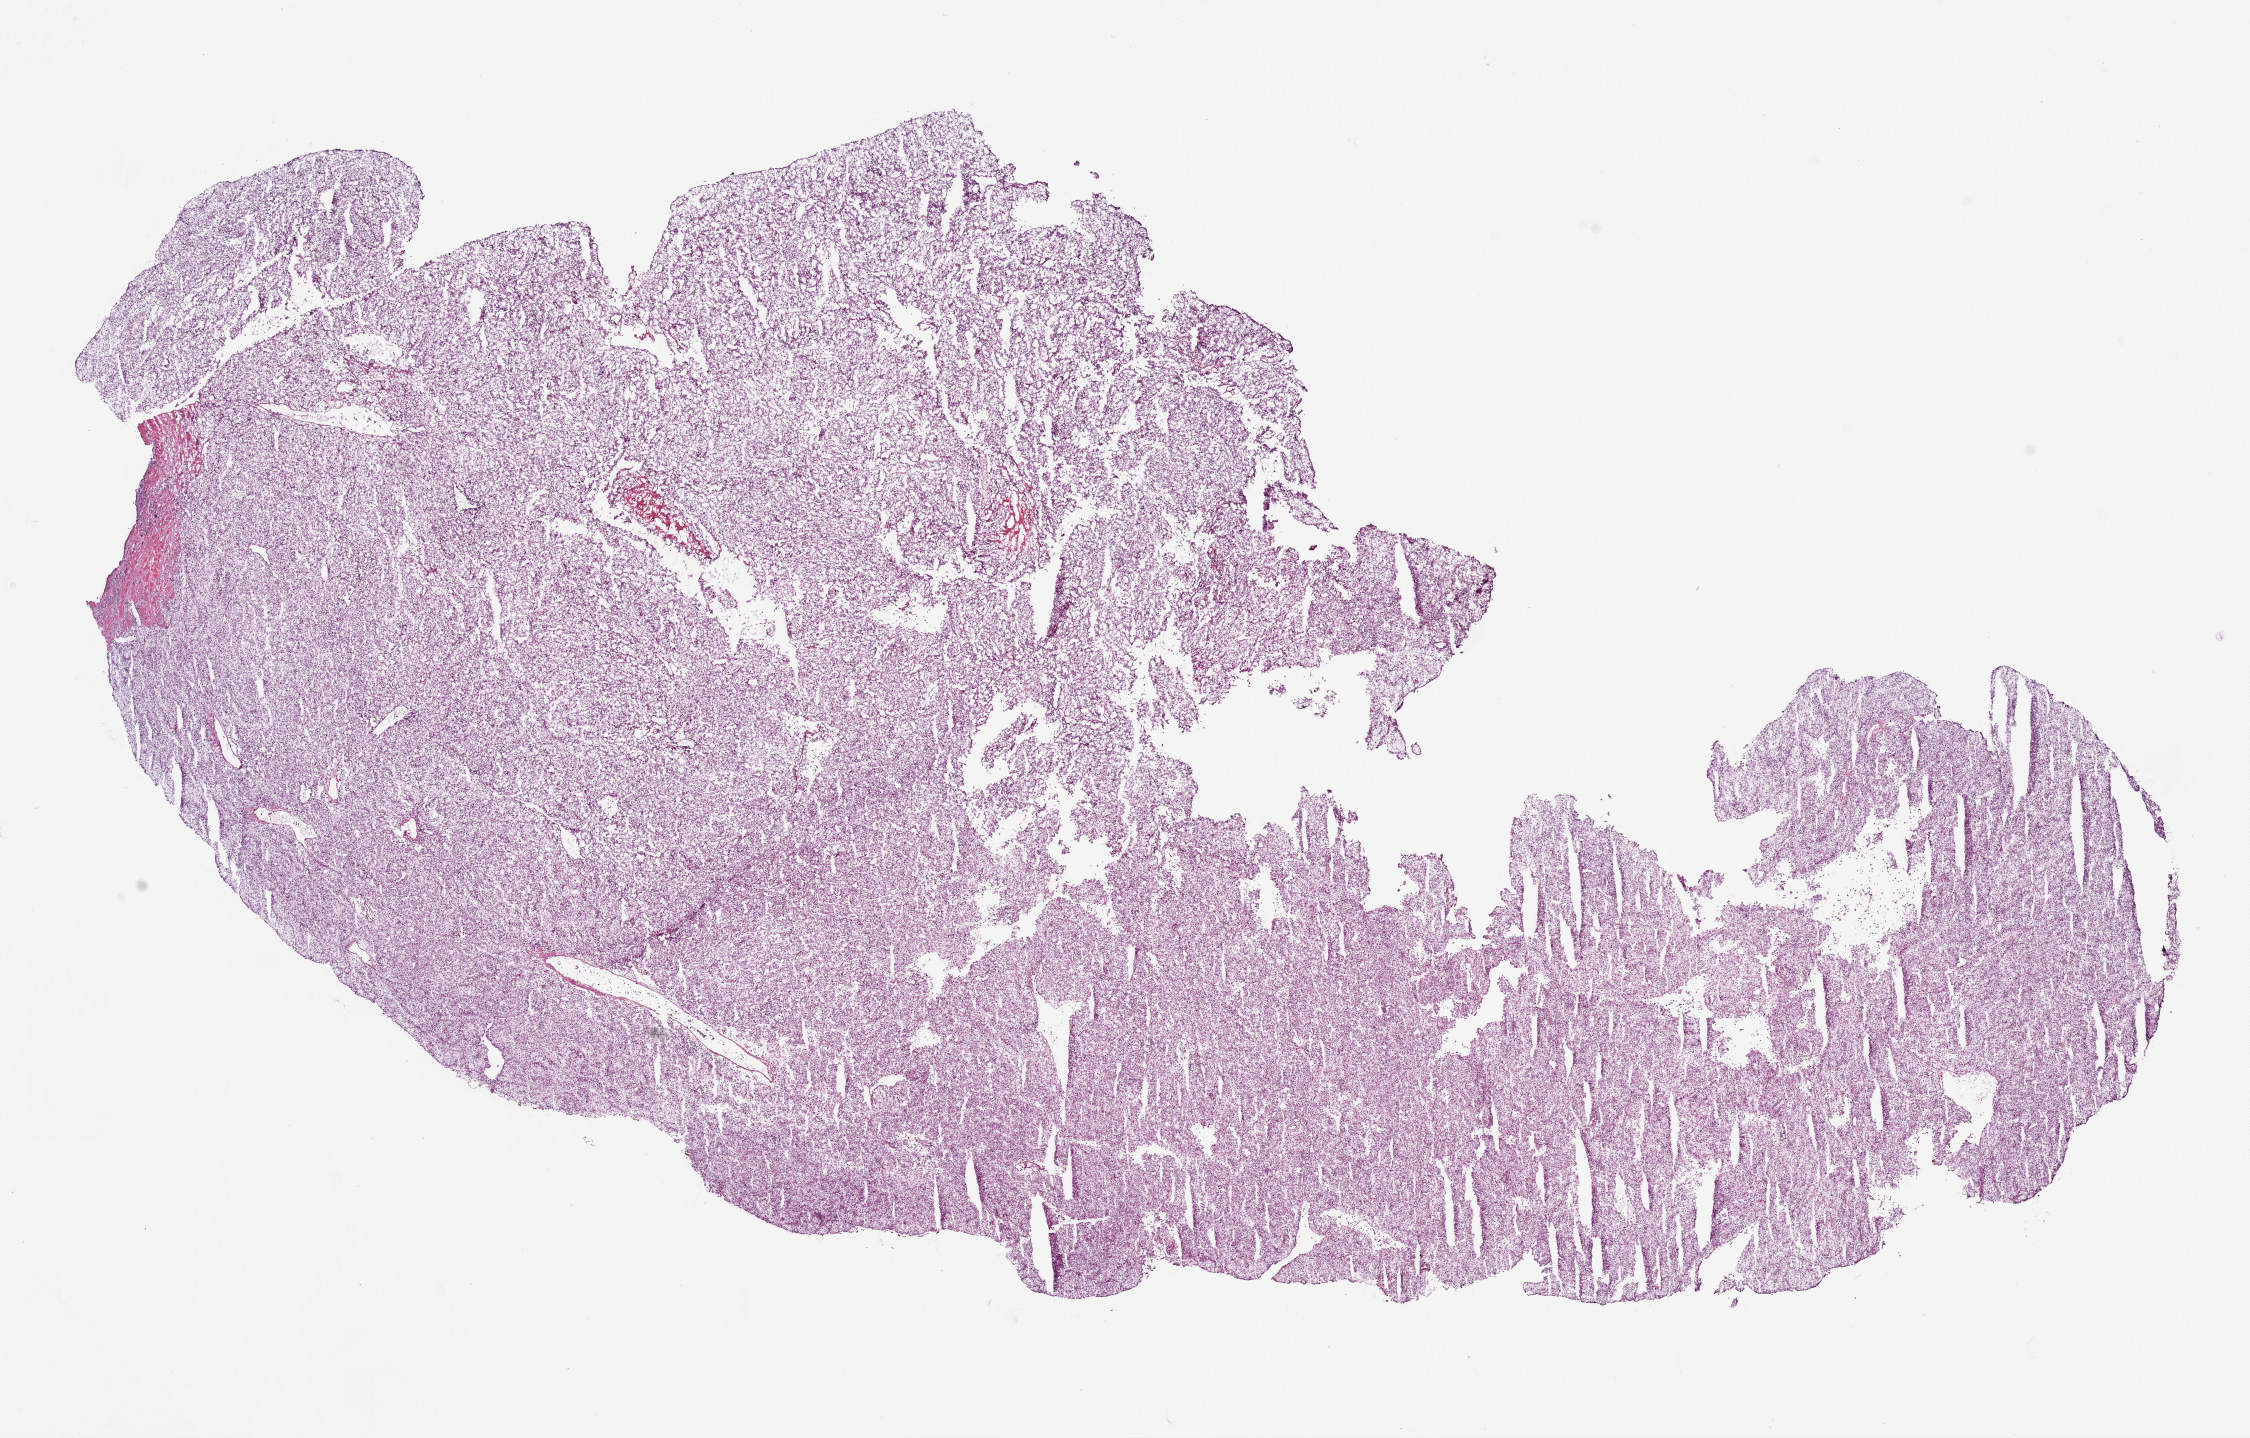
Whole-slide histology image, H&E-stained — shown as a low-resolution overview of the whole scanned area (about 18.1 x 11.5 mm, slide scanned at 20x), frozen section, kidney, primary tumour sample. Male, age 53 years at initial diagnosis. Histologic grade: G2 (moderately differentiated). Composition of this section per pathologist review: tumour cells 90%, tumour nuclei 90%, normal cells 0%, stromal cells 10%, necrosis 0%.
Histologic diagnosis: Clear cell adenocarcinoma, NOS. AJCC pathologic stage: I.